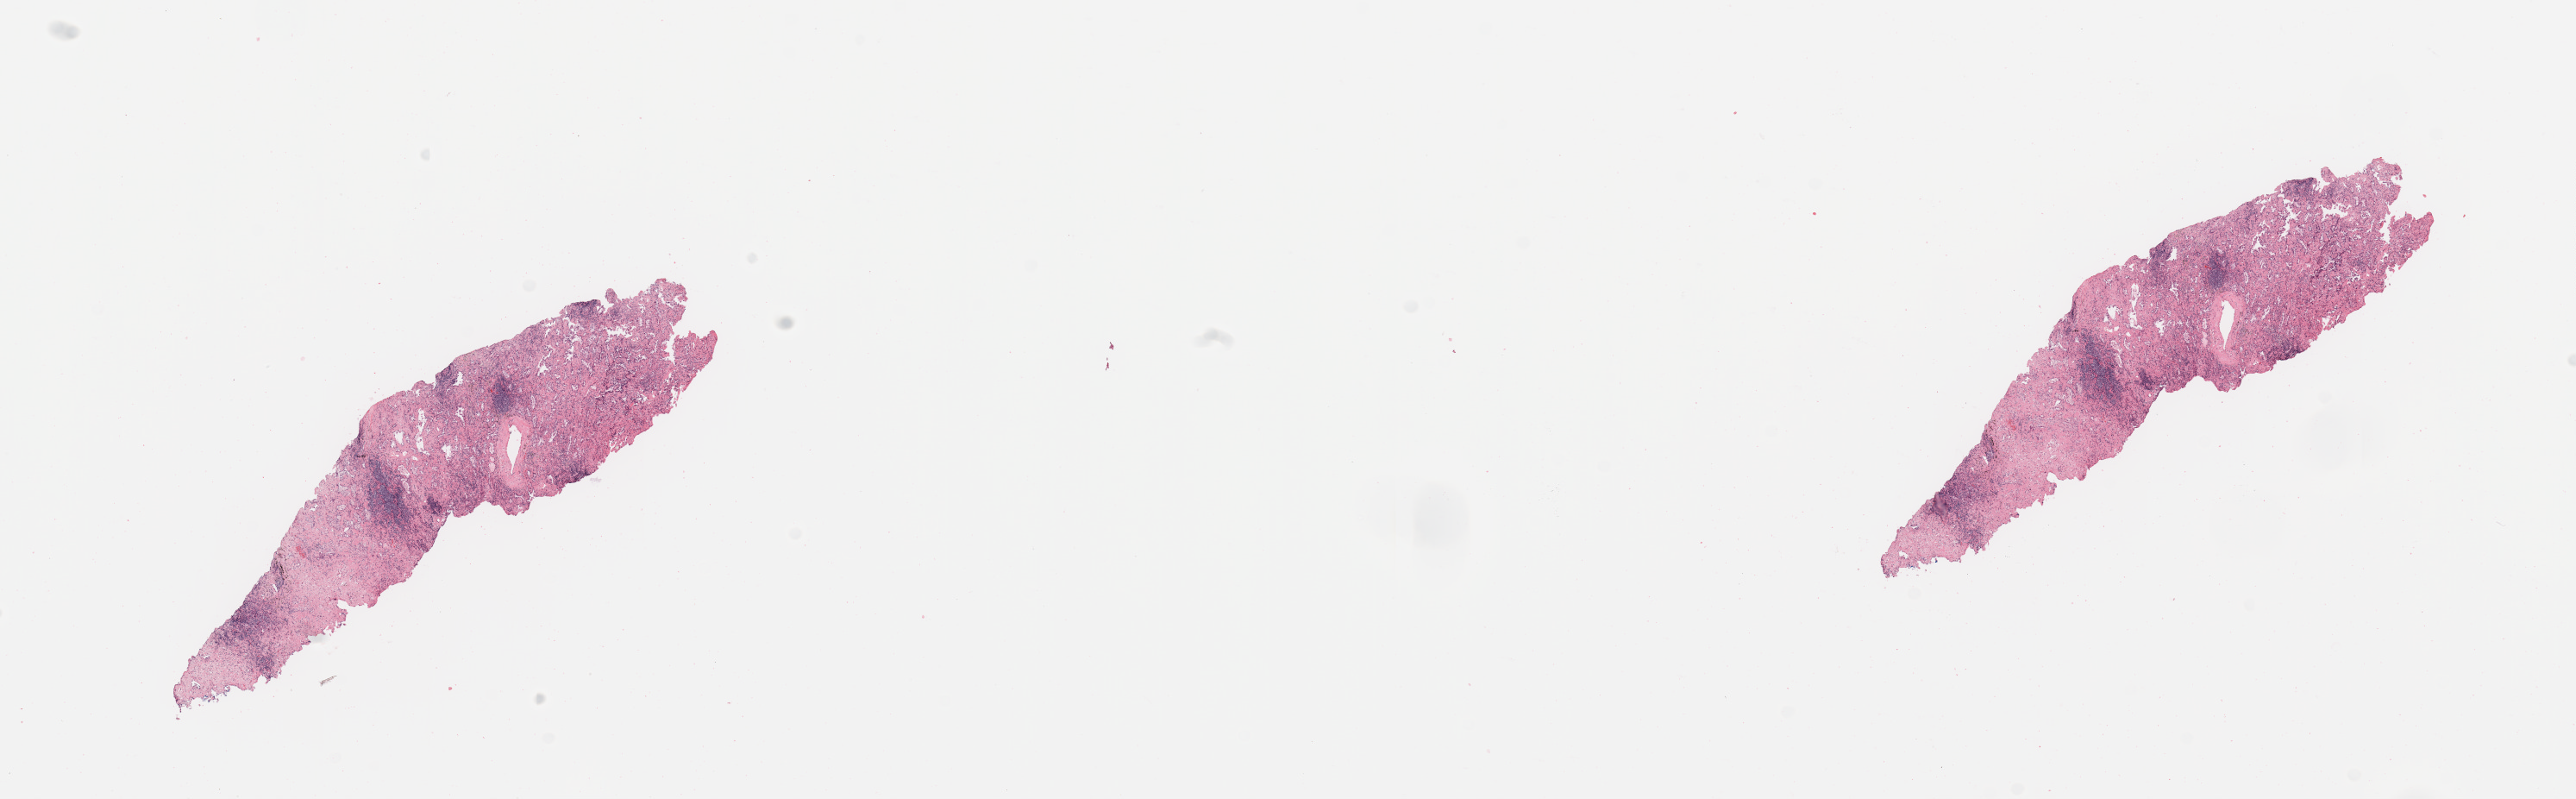
Digitized H&E tissue section (whole slide) — shown as a low-resolution overview of the whole scanned area (about 23.6 x 7.3 mm, from a 20x scan). Lung, tissue type not recorded.
Patient diagnosis (cohort enrolment): lung adenocarcinoma (lung).